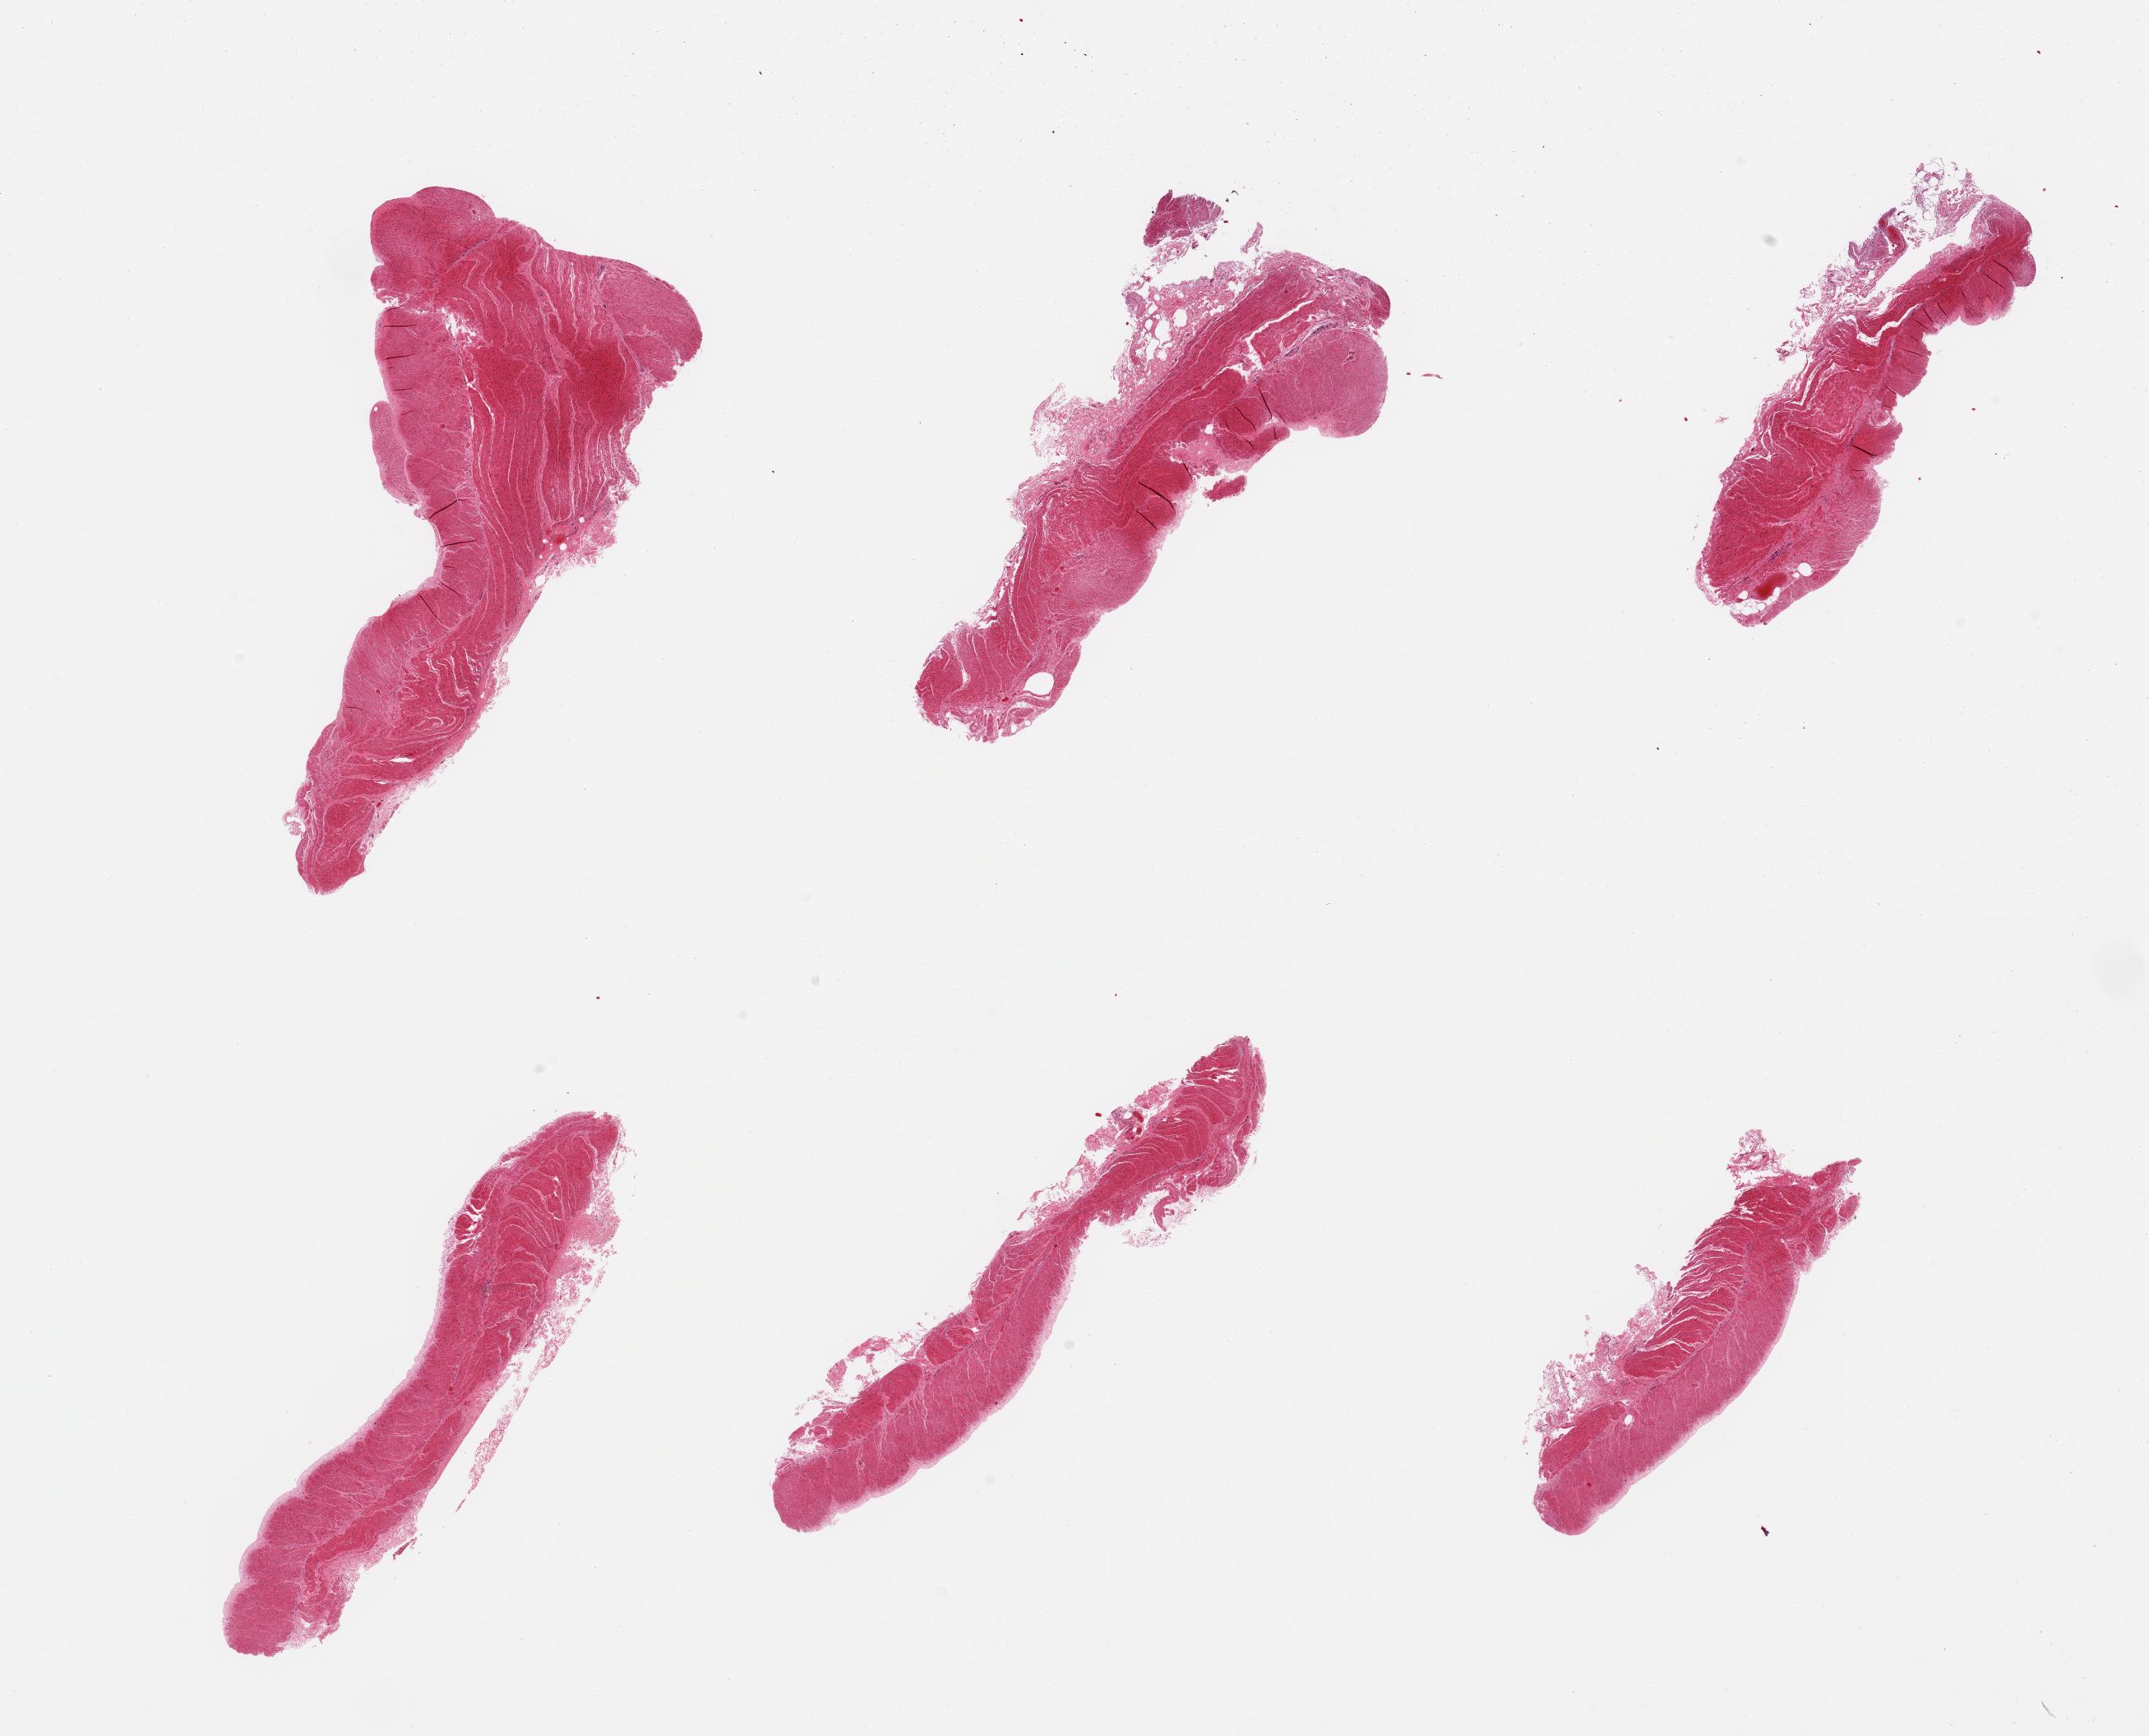
H&E whole-slide image, brightfield — a low-resolution overview of the entire scanned area, about 20.7 x 16.7 mm; PAXgene-fixed paraffin-embedded (PFPE) section; target tissue: sigmoid colon; tissue donor sample. Female donor.
Pathologist's review note for this sample: 6 pieces, confirmed target muscularis; few adherent rims of serosa up to ~0.6mm.